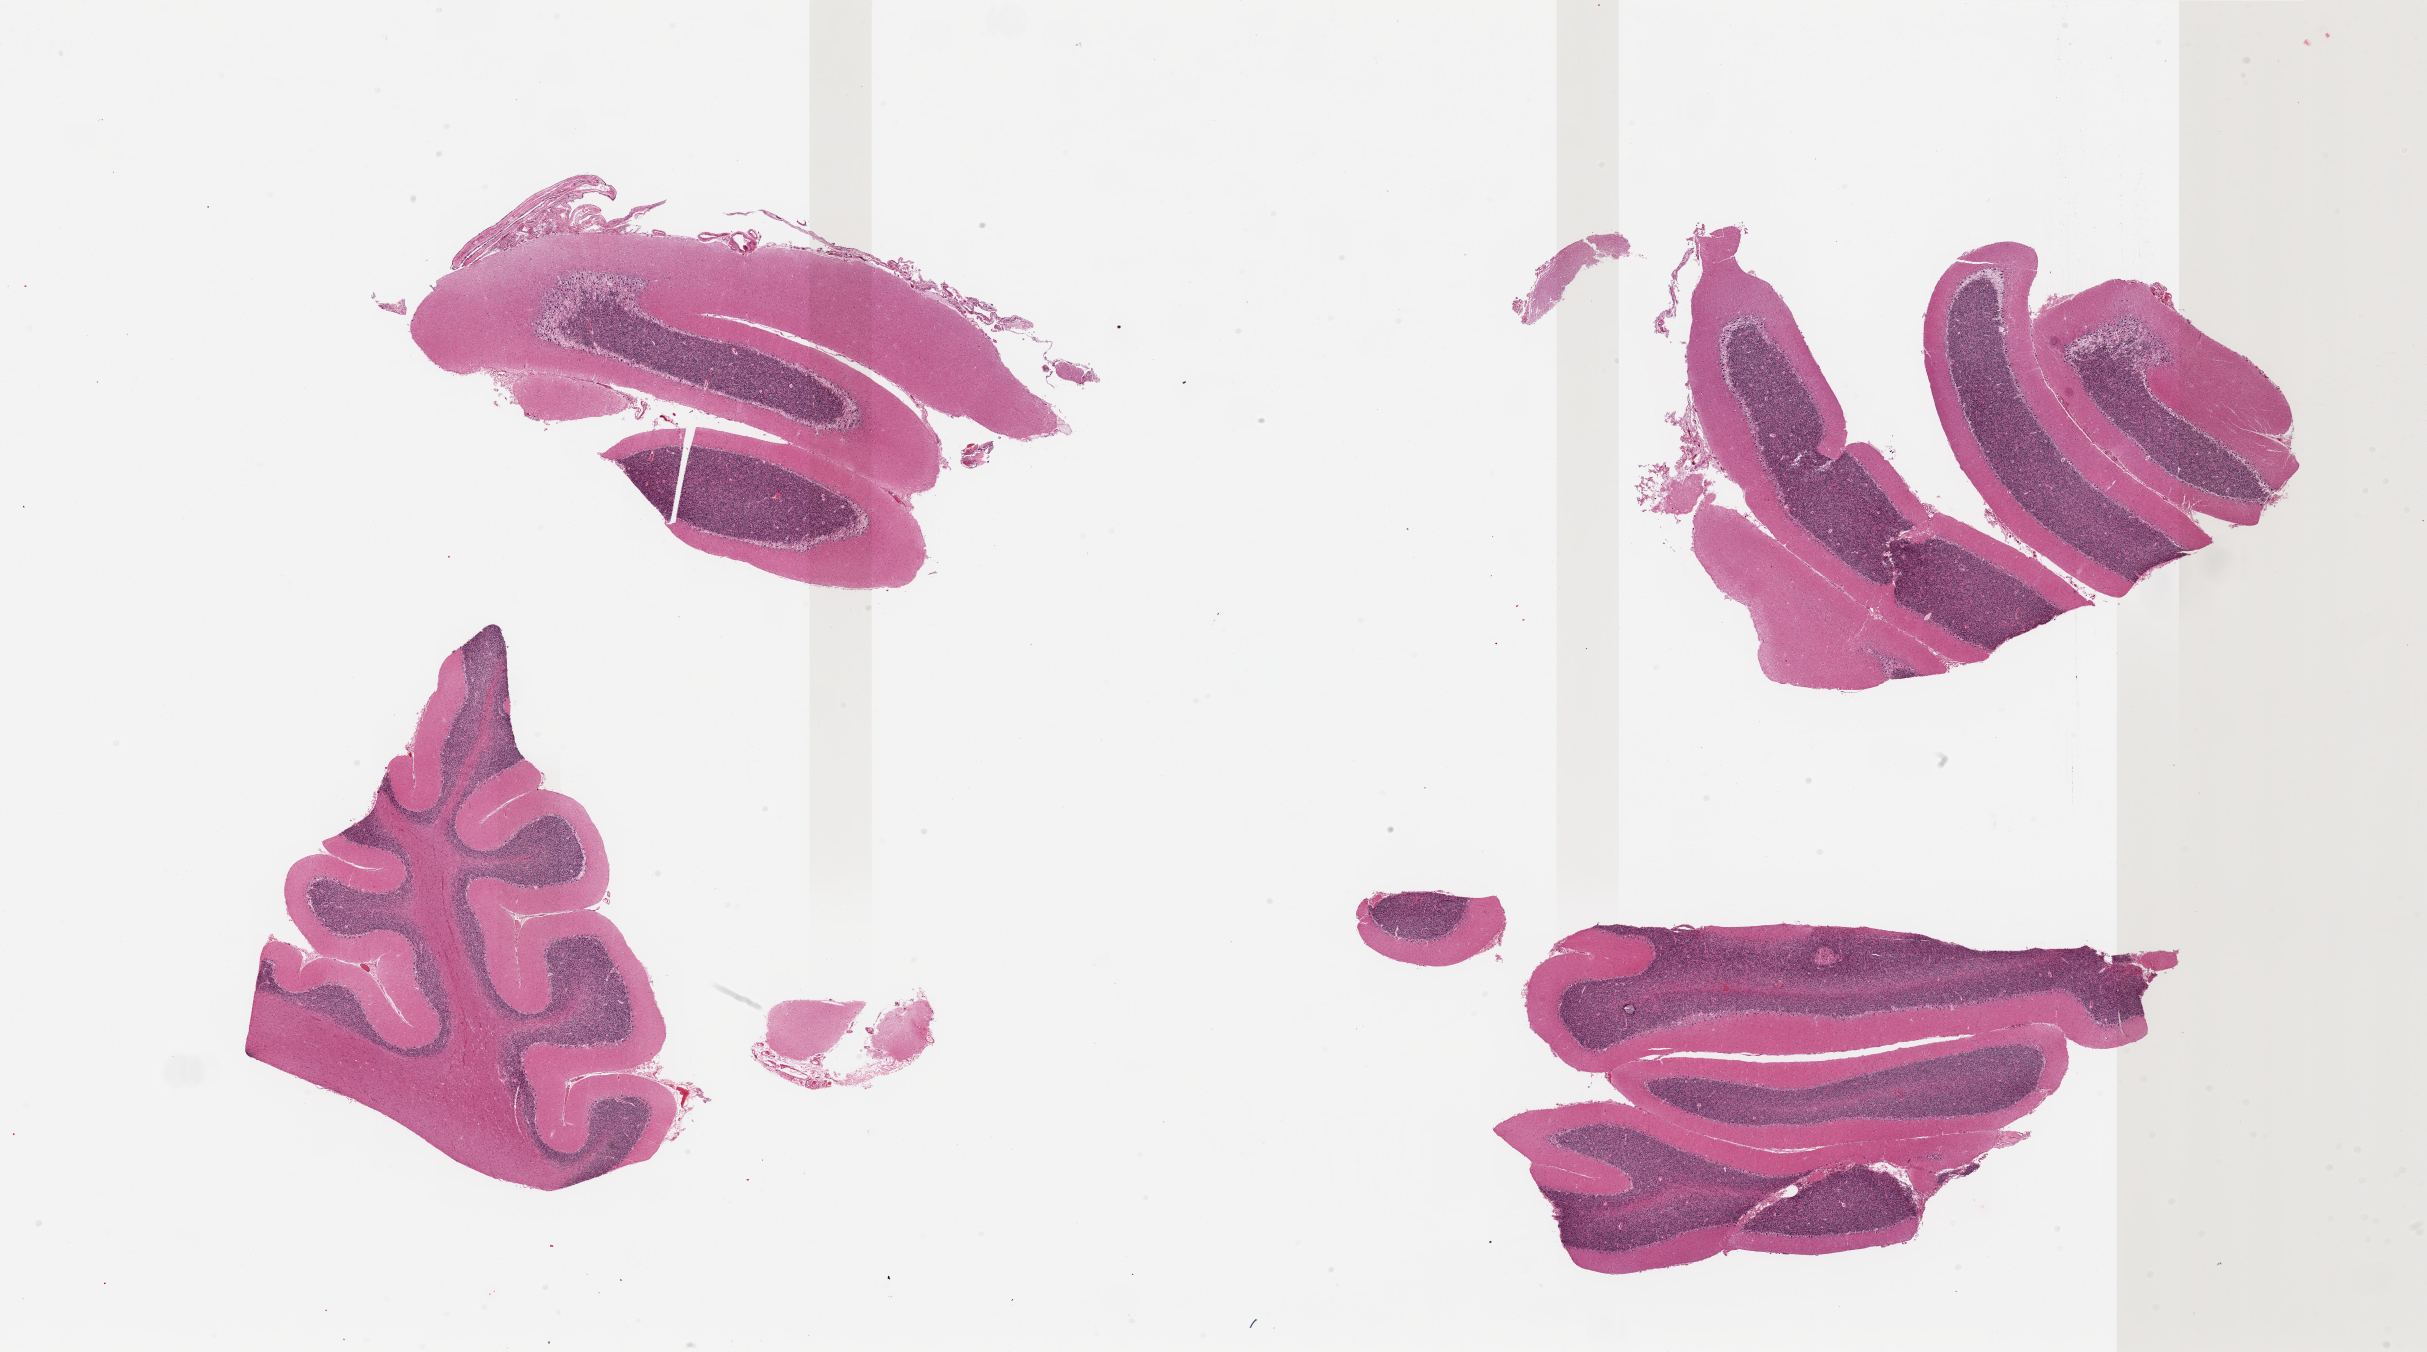
Digitized haematoxylin and eosin-stained section — shown as a low-resolution overview of the whole scanned area (about 38.4 x 21.4 mm, from a 20x scan). PAXgene-fixed paraffin-embedded (PFPE) section. Target tissue: cerebellum. Tissue donor sample. Donor: female.
Reviewer comment on this tissue sample: 4 pieces, no abnormalities.